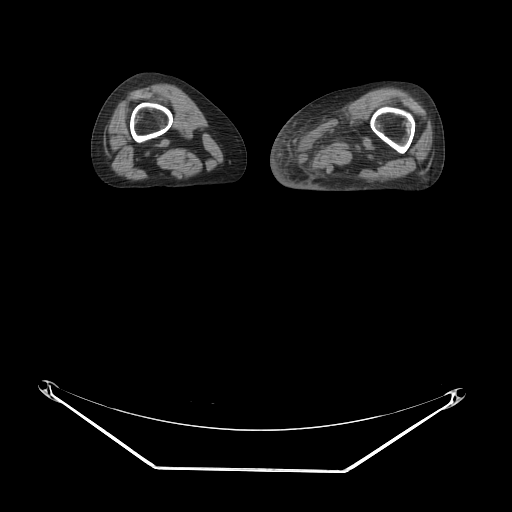
CT of an extremity soft-tissue mass (from a PET/CT study), one axial slice; slice 4 of 91 in the series (ordered by position); reconstruction kernel STANDARD; soft-tissue window (W 400 / L 40 HU); 3.75 mm slice thickness; 512 × 512 image matrix, field of view 500 × 500 mm. Female patient. Case-level facts recorded for this patient, not image findings: histological type: pleomorphic leiomyosarcoma; grade: high; site of the primary tumour: left thigh.
Outlined on this slice (expert contour drawn on MRI and transferred to this co-registered scan by the dataset authors):
- gross tumour volume including surrounding oedema: bounding box (x1, y1, x2, y2) in pixels: (306, 105, 382, 181)